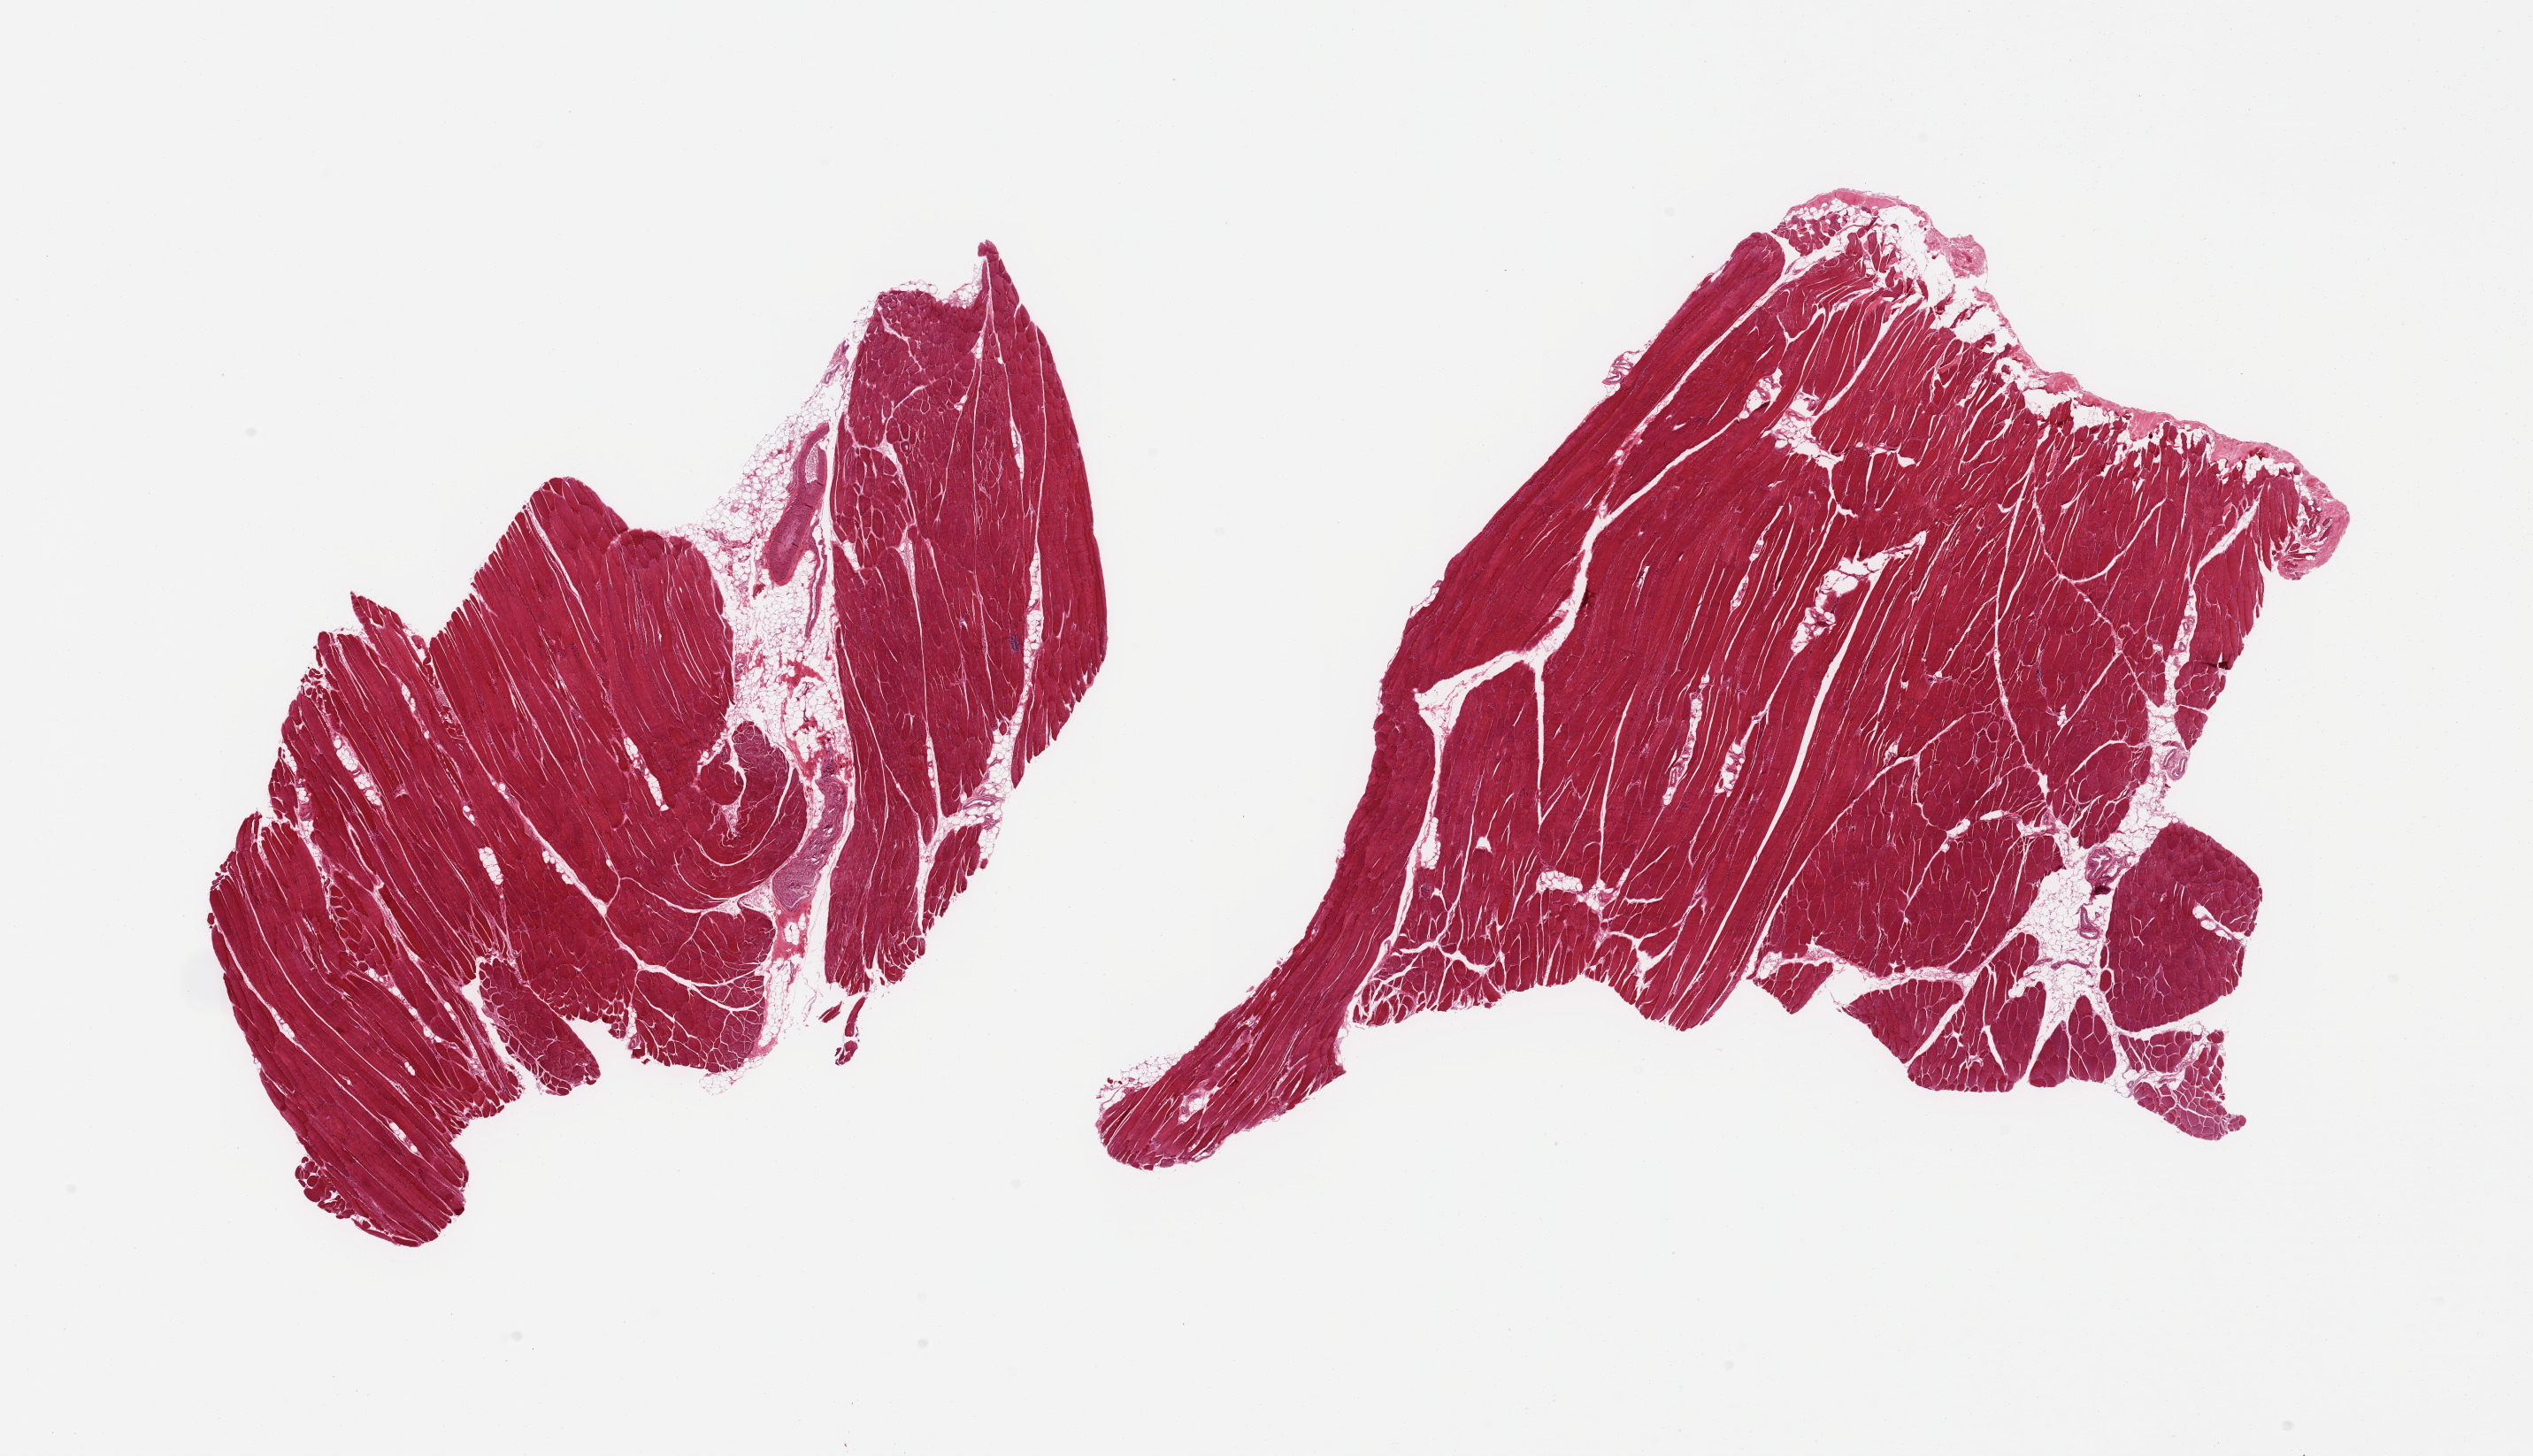
Digitized haematoxylin and eosin-stained section, a low-resolution overview of the entire scanned area, about 22.6 x 13.0 mm; PAXgene-fixed, paraffin-embedded tissue; sampled site (target tissue): skeletal muscle; donor tissue sample. Donor: female.
- pathologist's review note for this sample: 2 pieces: 1 has 10% neurovascular fatty tissue